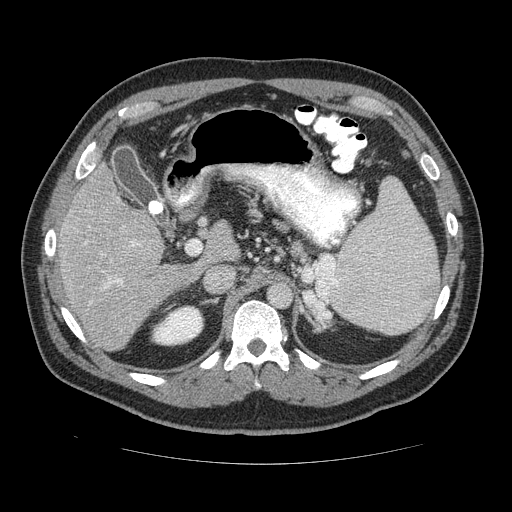
Contrast-enhanced abdominal CT (liver protocol), one axial slice; slice 78 of 113 in the series (ordered by position); reconstruction kernel STANDARD; soft-tissue window (W 400 / L 40 HU); 2.5 mm slice thickness; 512 × 512 image matrix, field of view 400 × 400 mm. Case-level facts recorded for this patient, not image findings: diagnosis: hepatocellular carcinoma (patient treated with transarterial chemoembolisation; whether this scan precedes or follows treatment is not stated here); TNM stage (as recorded): Stage-II; Child-Pugh class: B; tumour differentiation: moderately differentiated; tumour size: 4.8 cm.
Outlined on this slice (semi-automatically segmented with operator editing):
- liver parenchyma outside the tumour (the mass and vessels are separate outlines, so this box may not span the whole liver): box from (x=52, y=162) to (x=230, y=350) px
- liver vessels: (x=51, y=232)–(x=139, y=289)